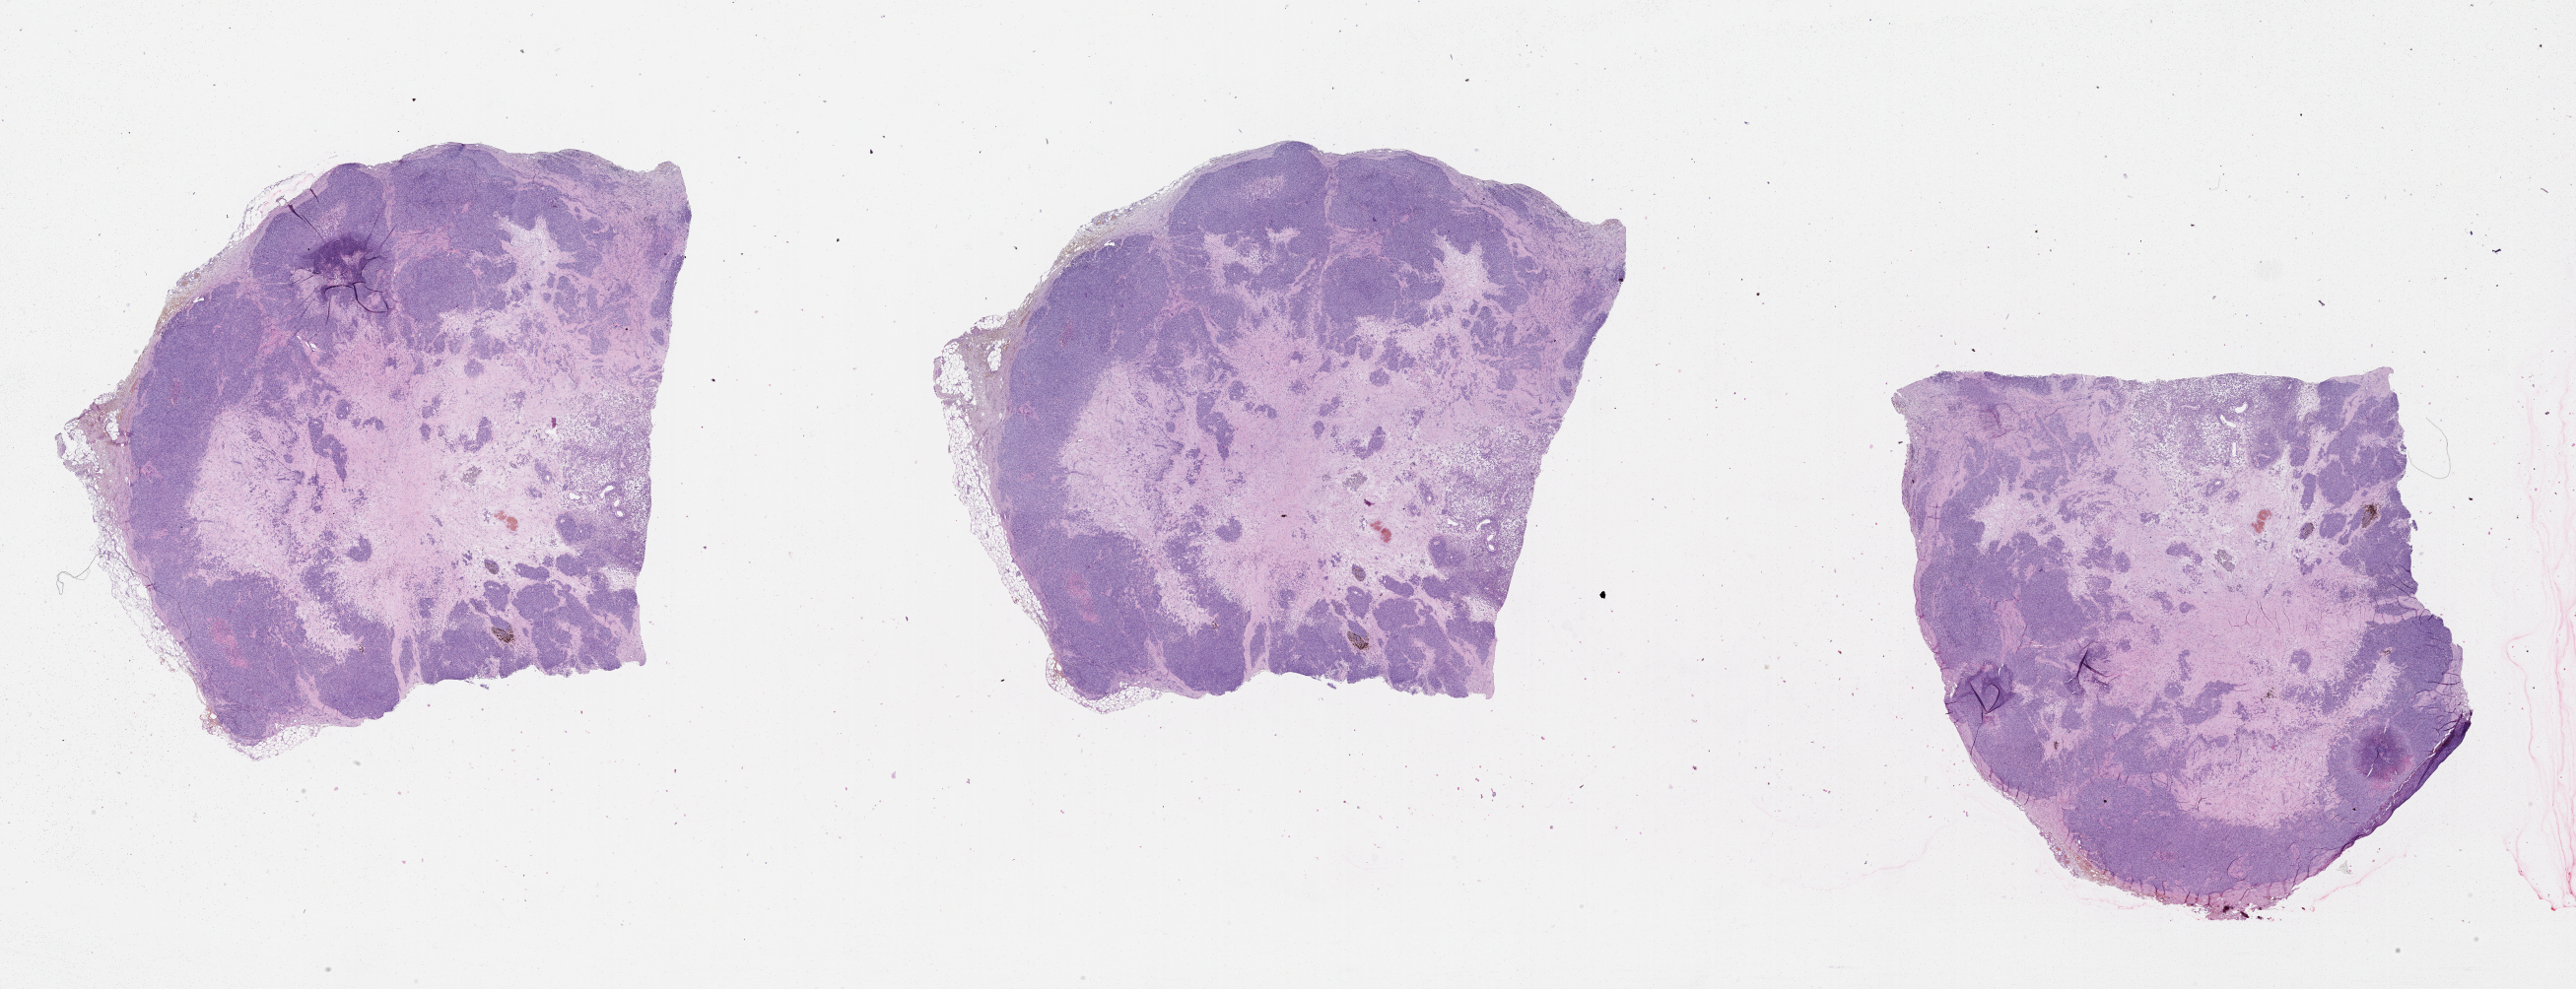
Hematoxylin and eosin (H&E) stained whole-slide image — a low-resolution overview of the entire scanned area, about 42.1 x 16.2 mm (slide scanned at 20x). Patient: male, age 83 years.
Patient diagnosis: Malignant melanoma, NOS.